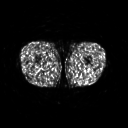
FDG PET of an extremity soft-tissue mass (from a PET/CT study), one axial slice. Position 219 of 267 along the scan axis. 3.27 mm slice thickness. 128 × 128 image matrix, field of view 500 × 500 mm. Male patient, age 27 years. Case-level facts recorded for this patient, not image findings: histological type: extraskeletal osteosarcoma; grade: high; site of the primary tumour: left adductur.
Structures marked on this image (expert contour drawn on MRI and transferred to this co-registered scan by the dataset authors):
- gross tumour volume (mass): bounding box (x1, y1, x2, y2) in pixels: (70, 62, 89, 70)